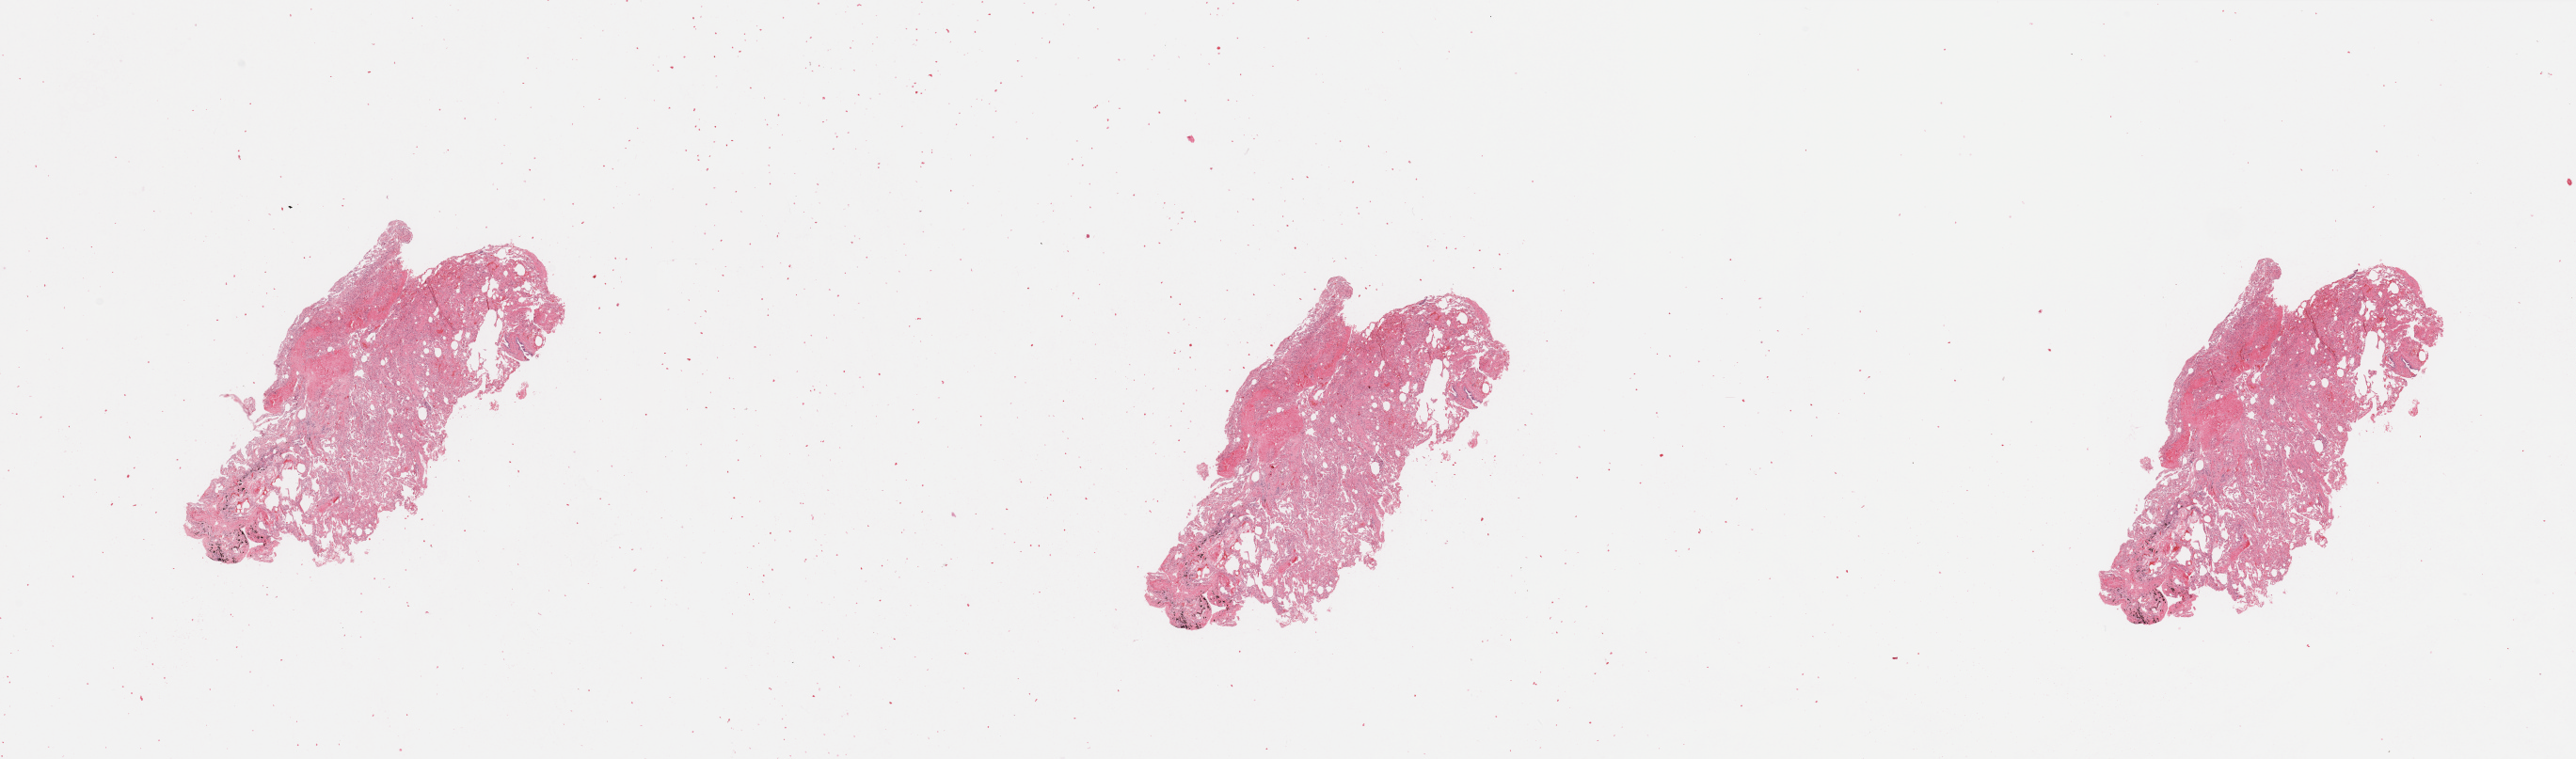
Digitized H&E-stained tissue section (whole slide) — whole scanned area (about 43.3 x 12.8 mm) shown as a low-resolution overview; normal (non-tumour) tissue sample, sampled site: lung. Male, 66 y/o.
This section: normal (non-tumour) tissue from the same patient. Patient diagnosis: Adenocarcinoma, NOS.